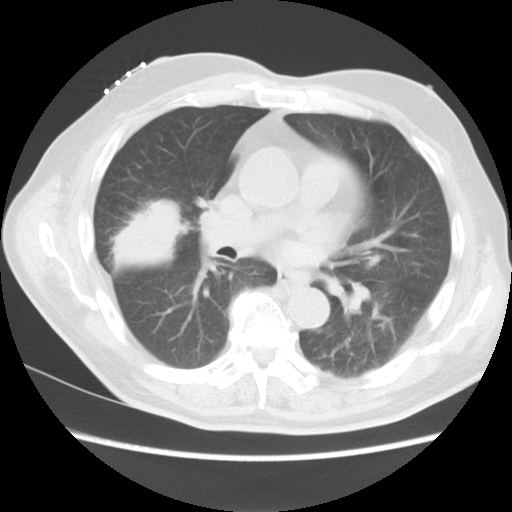
Chest CT, one axial slice; slice 4 of 15 in the series (ordered by position); reconstruction kernel STANDARD; 120 kVp; lung window (W 1500 / L -600 HU); 5 mm slice thickness; 512 × 512 image matrix, field of view 350 × 350 mm. Male patient, age 68 years. Case-level facts recorded for this patient, not image findings: clinical TNM (as recorded): T4 N3 M0.
Structures marked on this image (rectangle marked by the reading radiologist):
- lung tumour (recorded histology: squamous cell carcinoma): box from (x=109, y=191) to (x=192, y=280) px